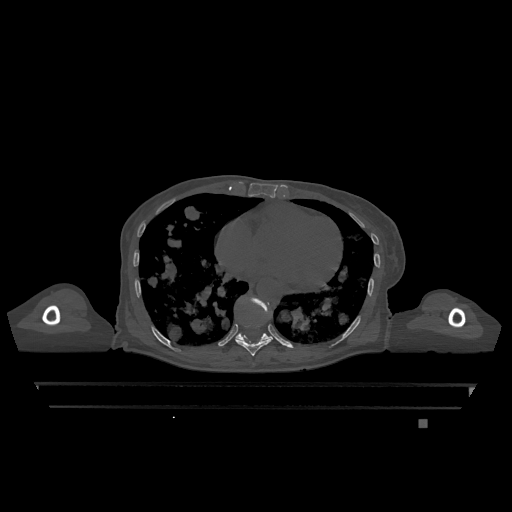
CT including the spine, one axial slice. Position 675 of 1317 along the scan axis. Bone window (W 1800 / L 400 HU). 512 × 512 image matrix. Female patient, age 74 years. Case-level facts recorded for this patient, not image findings: primary cancer: lung; vertebrae with lytic lesions (as recorded): T1, T4, T5, T6, L4, L5.
Structures marked on this image (semi-automatically segmented with operator editing):
- T10 vertebra: bounding box (x1, y1, x2, y2) in pixels: (235, 297, 273, 341)
- T9 vertebra: (236, 318, 272, 356)